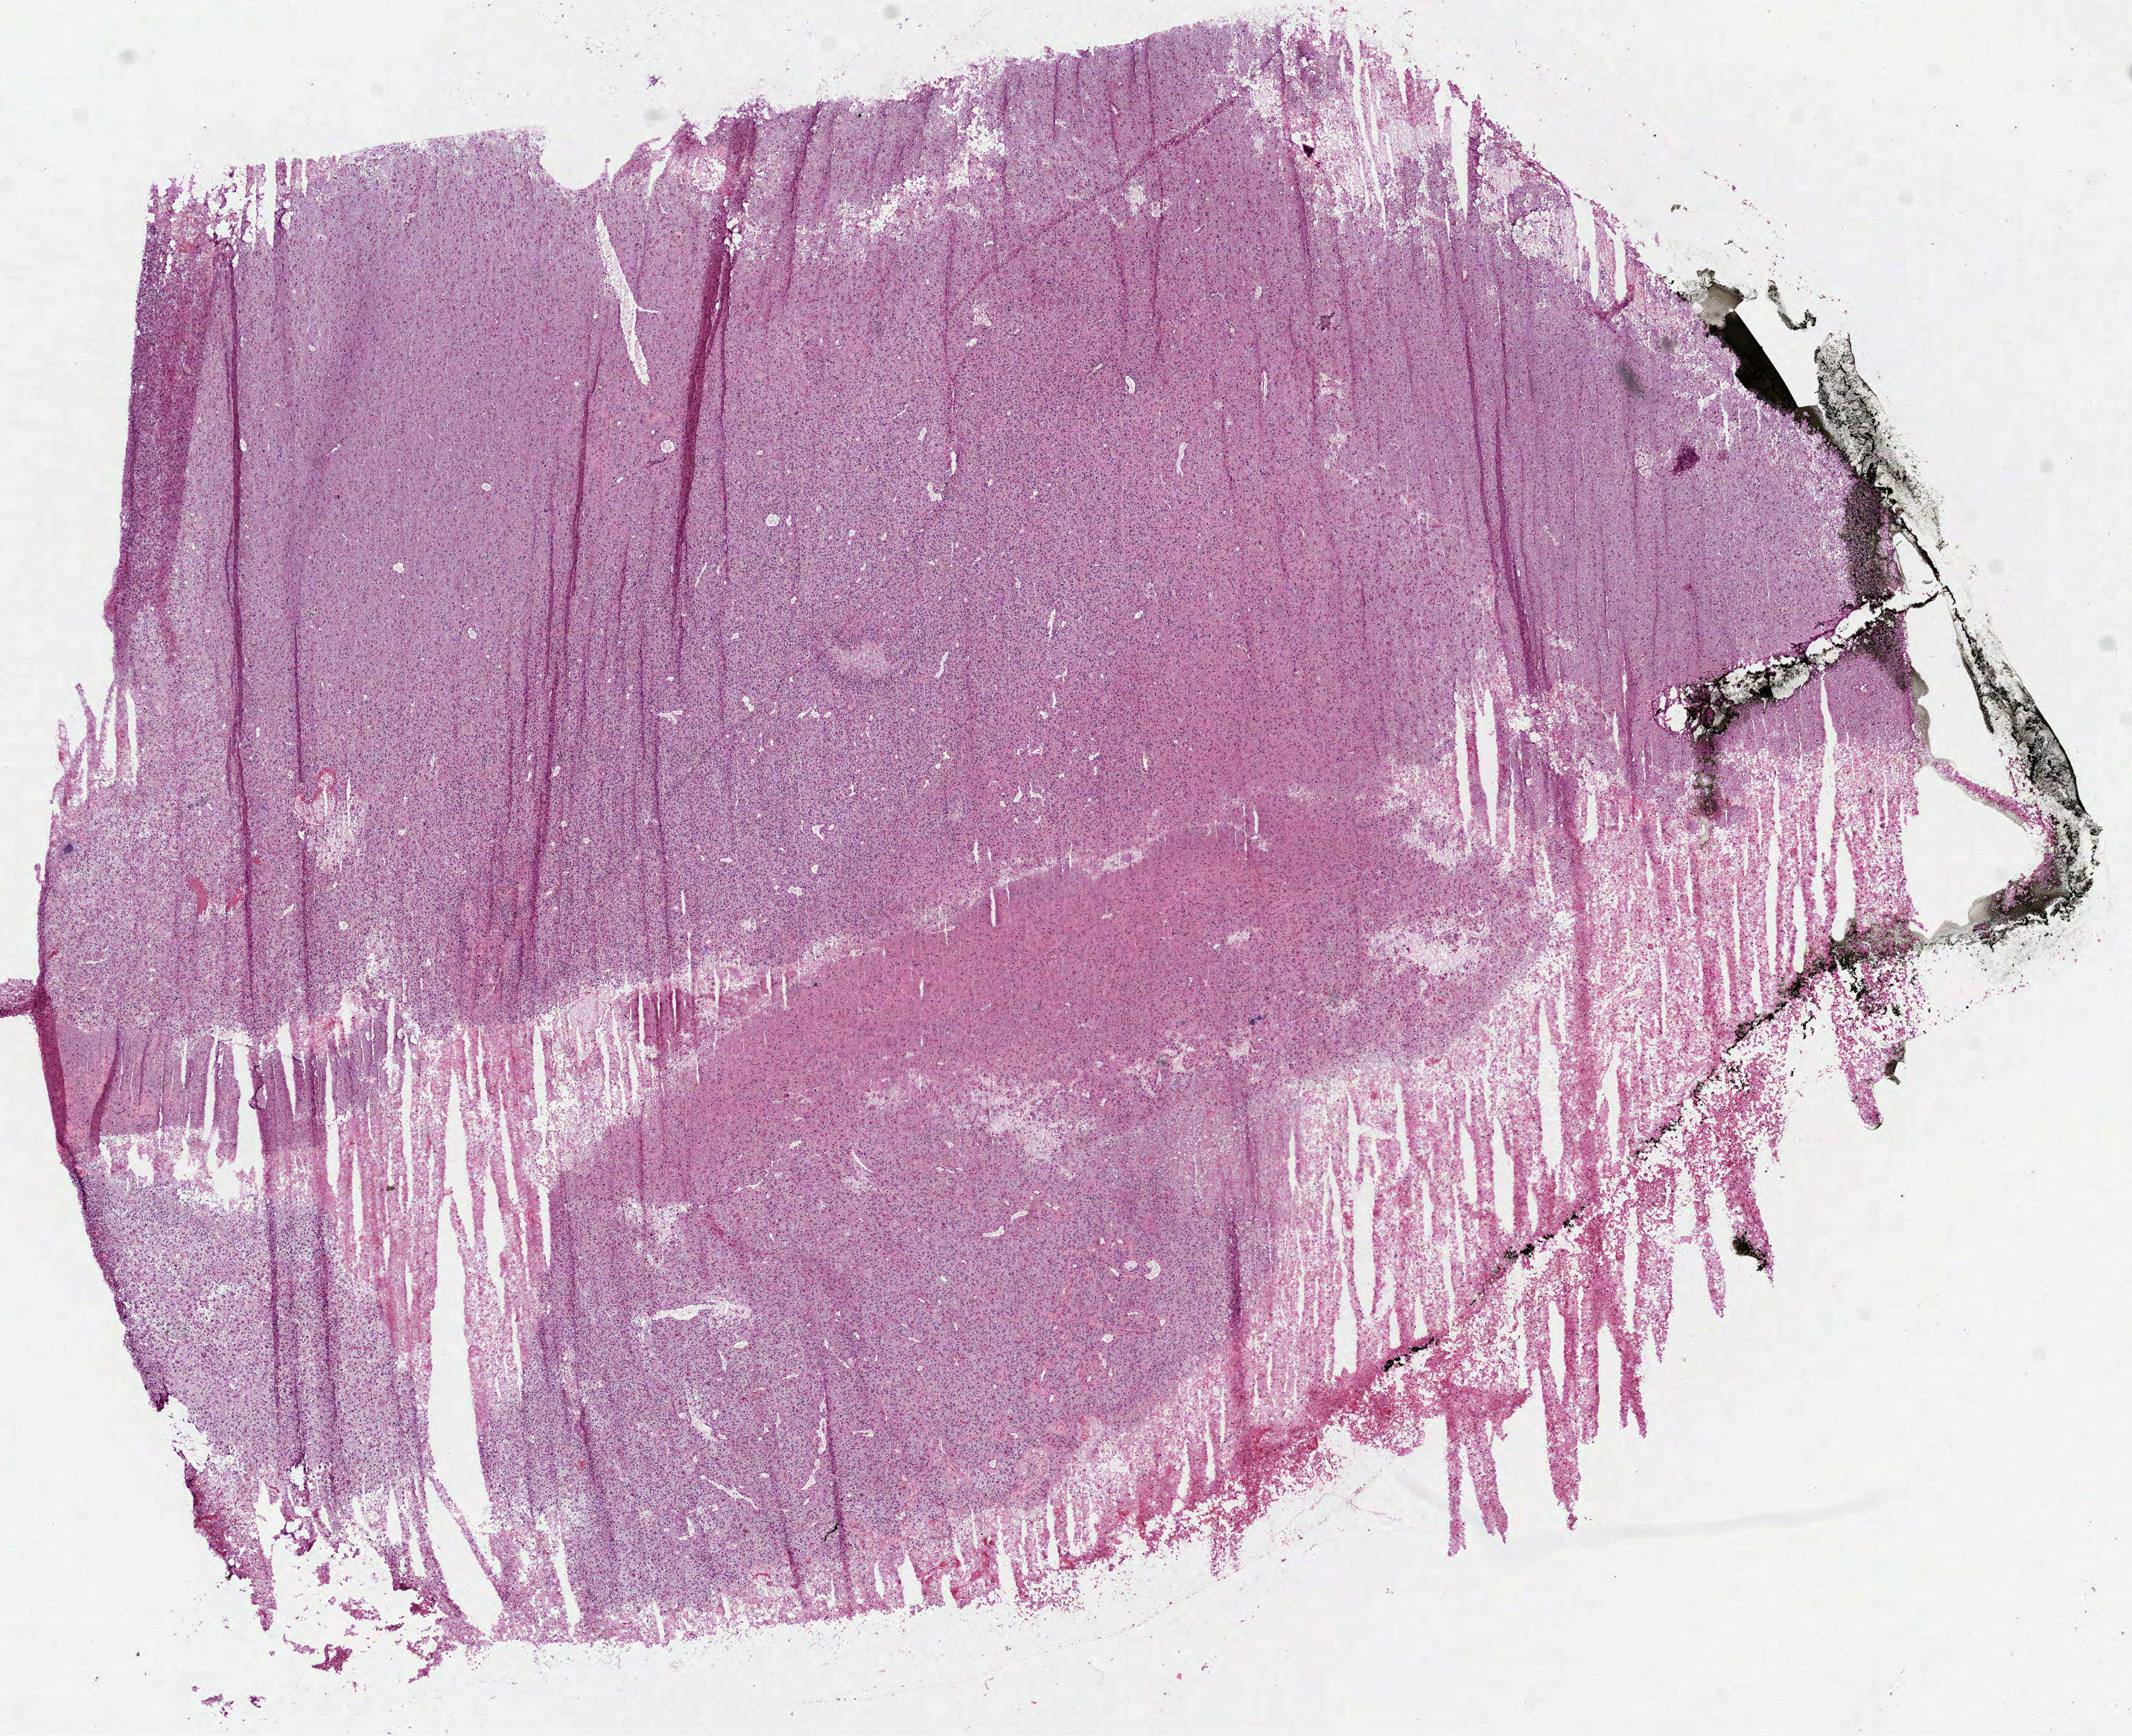
Whole-slide histology image, H&E-stained, shown as a low-resolution overview of the whole scanned area (about 11.5 x 9.4 mm, acquisition: 40x scan); frozen section; brain, primary tumour sample. Male, age 67 years at initial diagnosis. Slide review estimates, as recorded: tumour cells 82%, tumour nuclei 80%, normal cells 0%, stromal cells 0%, necrosis 18%.
- pathologic diagnosis: Glioblastoma